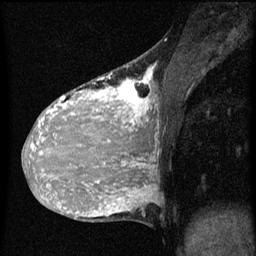
Breast MRI (dynamic contrast-enhanced), one sagittal slice; slice 25 of 60 in the series (ordered by position); dynamic contrast-enhanced series, image 2 of 3 at this slice position (ordered by acquisition); 1.5 T; TE 4.2 ms, TR 8 ms; 2 mm slice thickness; 256 × 256 image matrix, field of view 180 × 180 mm. Patient: female, 36 years.
Outlined on this slice (semi-automatic segmentation, software-assisted and operator-edited):
- analysis volume of interest (the breast-tissue region the enhancement analysis was run in; not a lesion): bounding box [x1, y1, x2, y2] px = [32, 68, 159, 161]
- tumour enhancement mask (voxels above the 70 % enhancement threshold inside the analysis volume of interest): [32, 68, 155, 161]